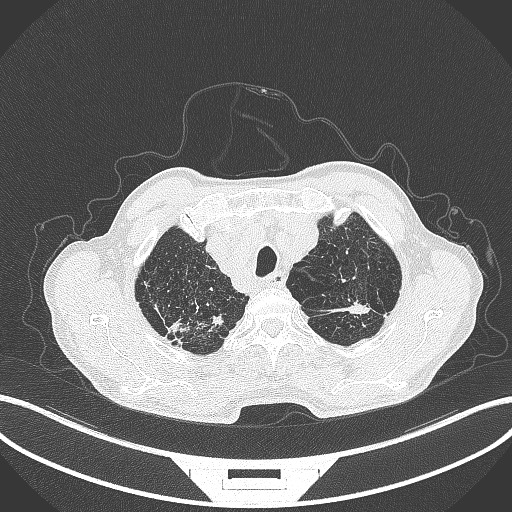
Chest CT, one axial slice. Slice 386 of 463 in the series (ordered by position). Reconstruction kernel B70f. Lung window (W 1500 / L -600 HU). 1 mm slice thickness. 512 × 512 image matrix, field of view 400 × 400 mm. Male patient, age 74 years. Case-level facts recorded for this patient, not image findings: clinical TNM (as recorded): T2a N1 M0.
Outlined on this slice (rectangle marked by the reading radiologist):
- lung tumour (recorded histology: adenocarcinoma): bounding box <328,296,373,318> (left, top, right, bottom; pixels)